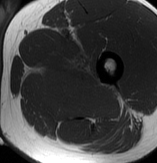
MRI of an extremity soft-tissue mass, one axial slice; slice 53 of 70 in the series (ordered by position); MR volume resampled by the dataset authors to the PET/CT grid (not the native acquisition matrix); 3.27 mm slice thickness; 157 × 163 image matrix, field of view 153 × 159 mm. Male patient. Case-level facts recorded for this patient, not image findings: histological type: extraskeletal osteosarcoma; grade: high; site of the primary tumour: left adductur.
Structures marked on this image (expert contour drawn on MRI and transferred to this co-registered scan by the dataset authors):
- gross tumour volume (mass): bounding box [x1, y1, x2, y2] px = [31, 53, 121, 121]